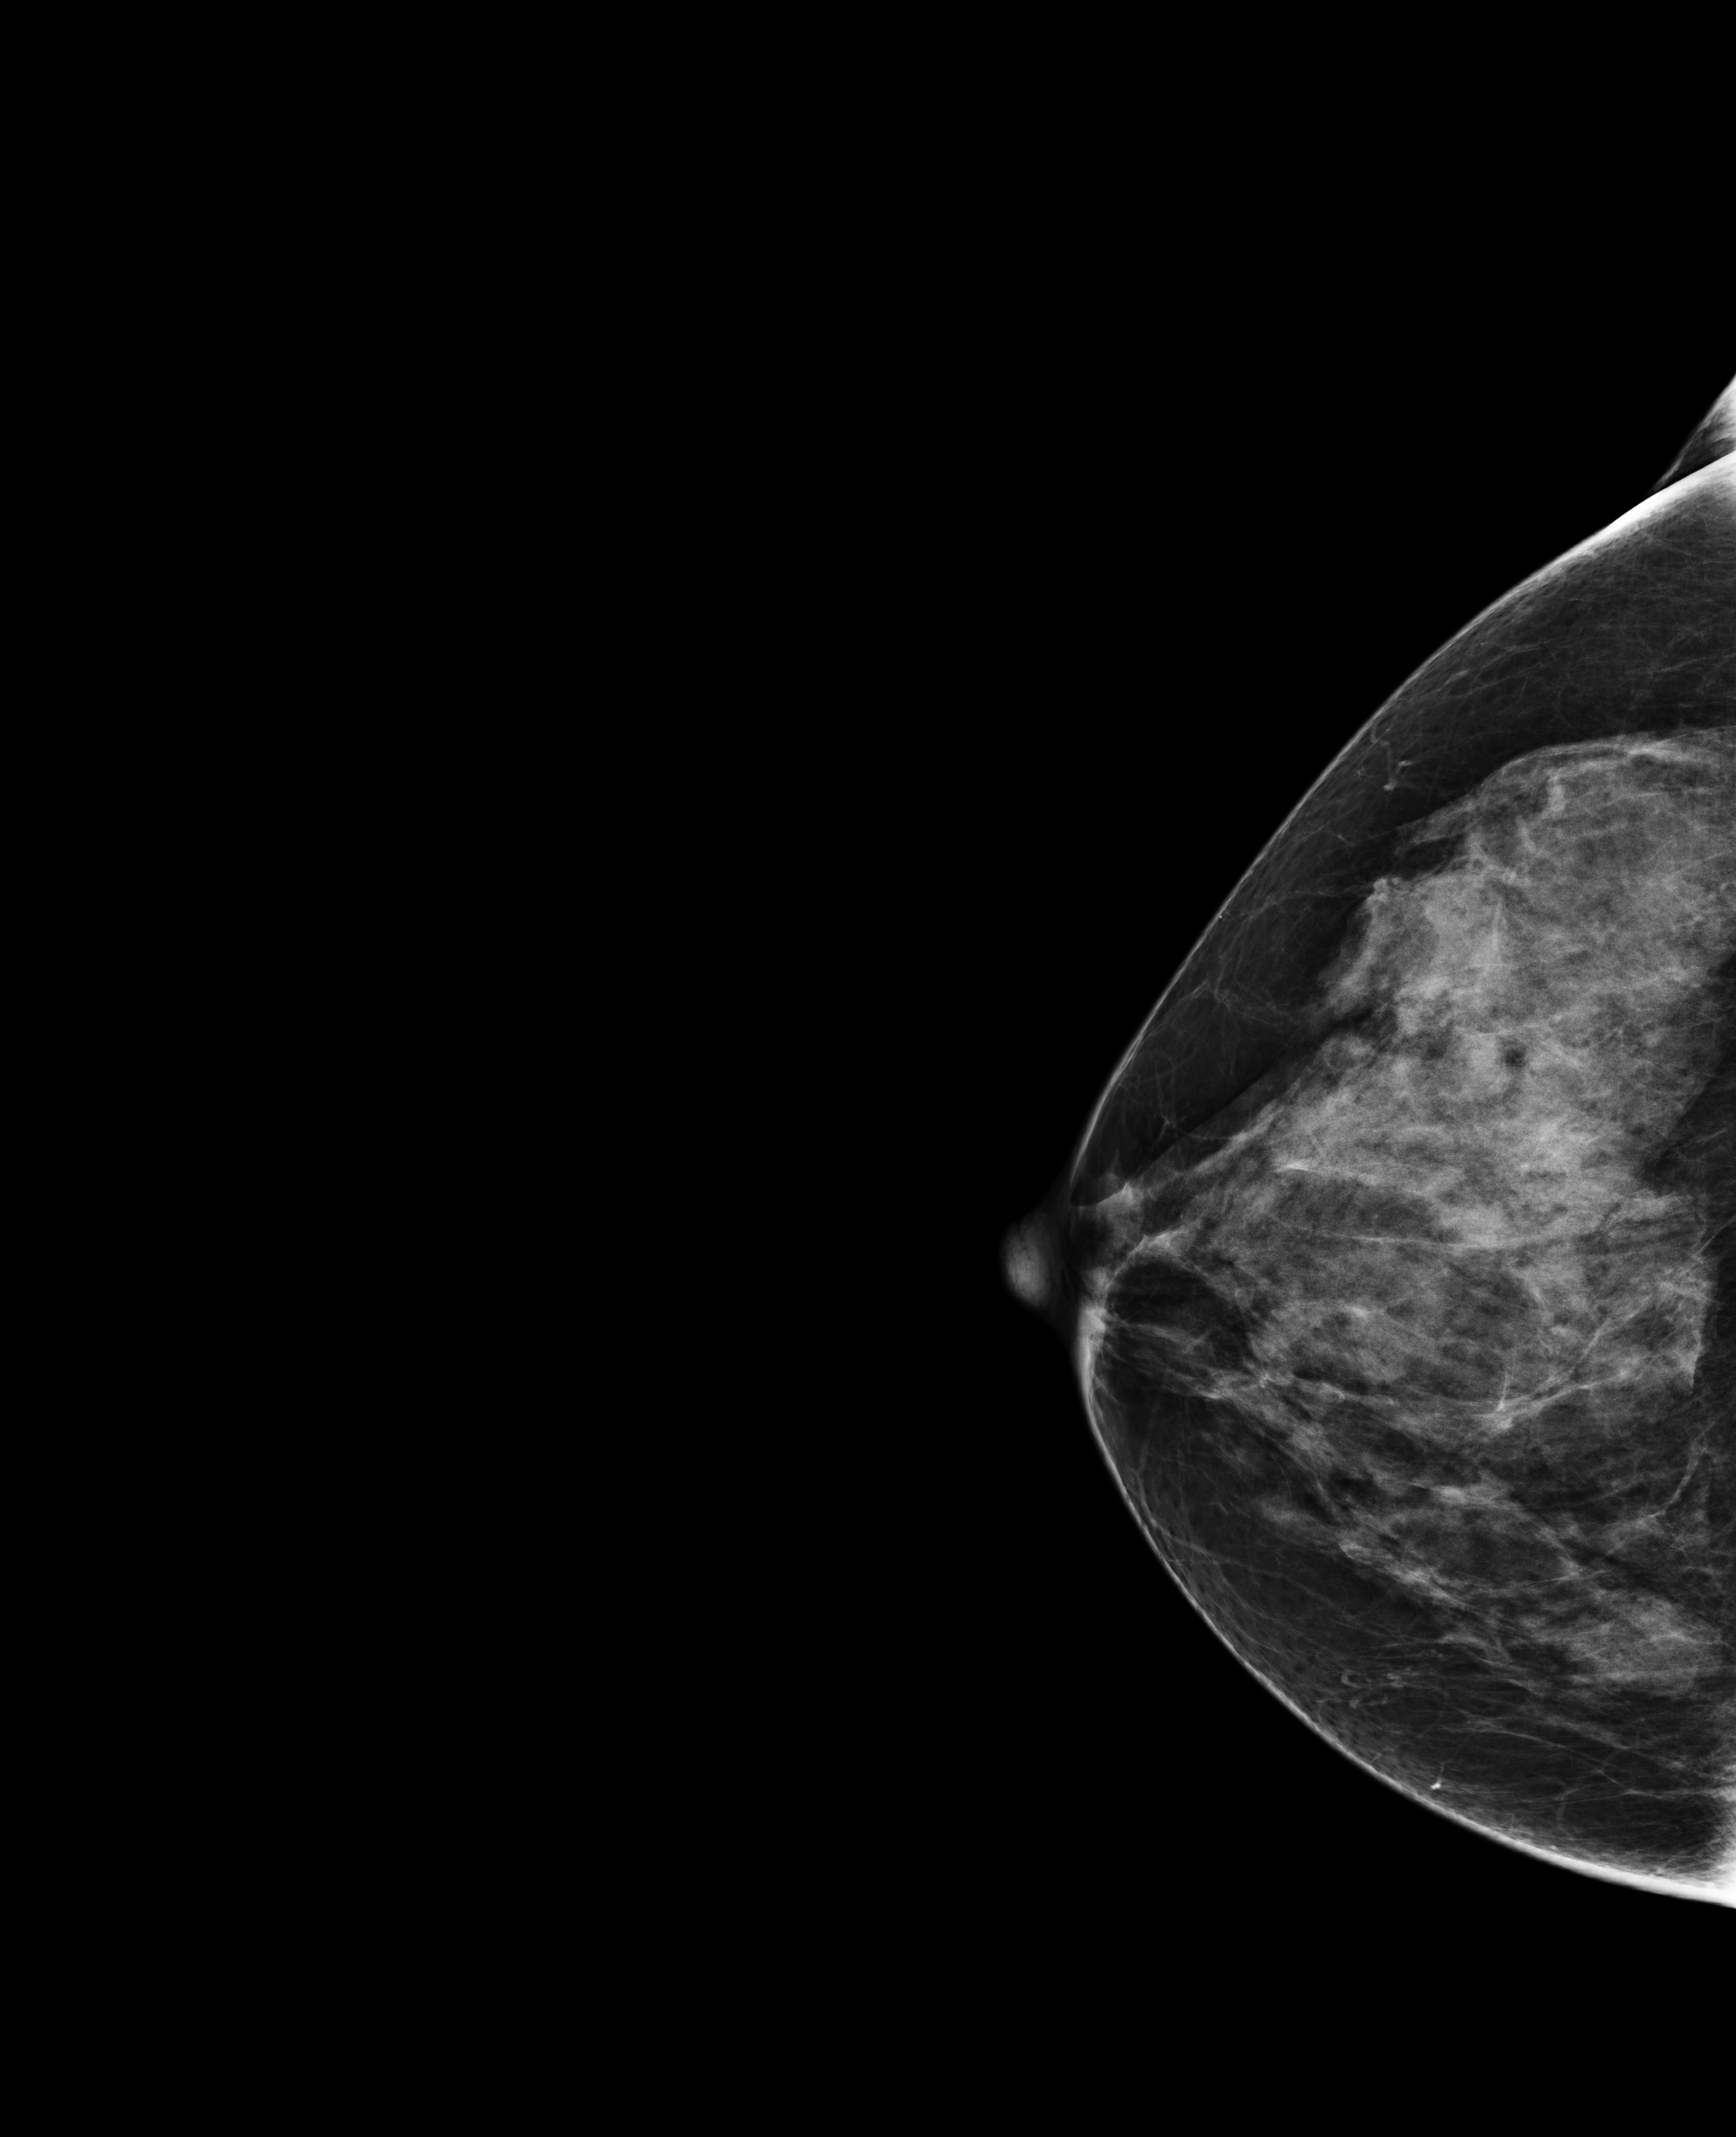
Full-field digital mammogram (FFDM); right breast; CC view; screening examination; compressed breast thickness 61 mm; system: Selenia Dimensions. Patient: female, 50 years.
Breast density at the screening exam (both breasts): extremely dense (BI-RADS density category d). Final BI-RADS assessment for this screening round (tomosynthesis exam, both breasts): category 1. Recall: no recall after this screen.